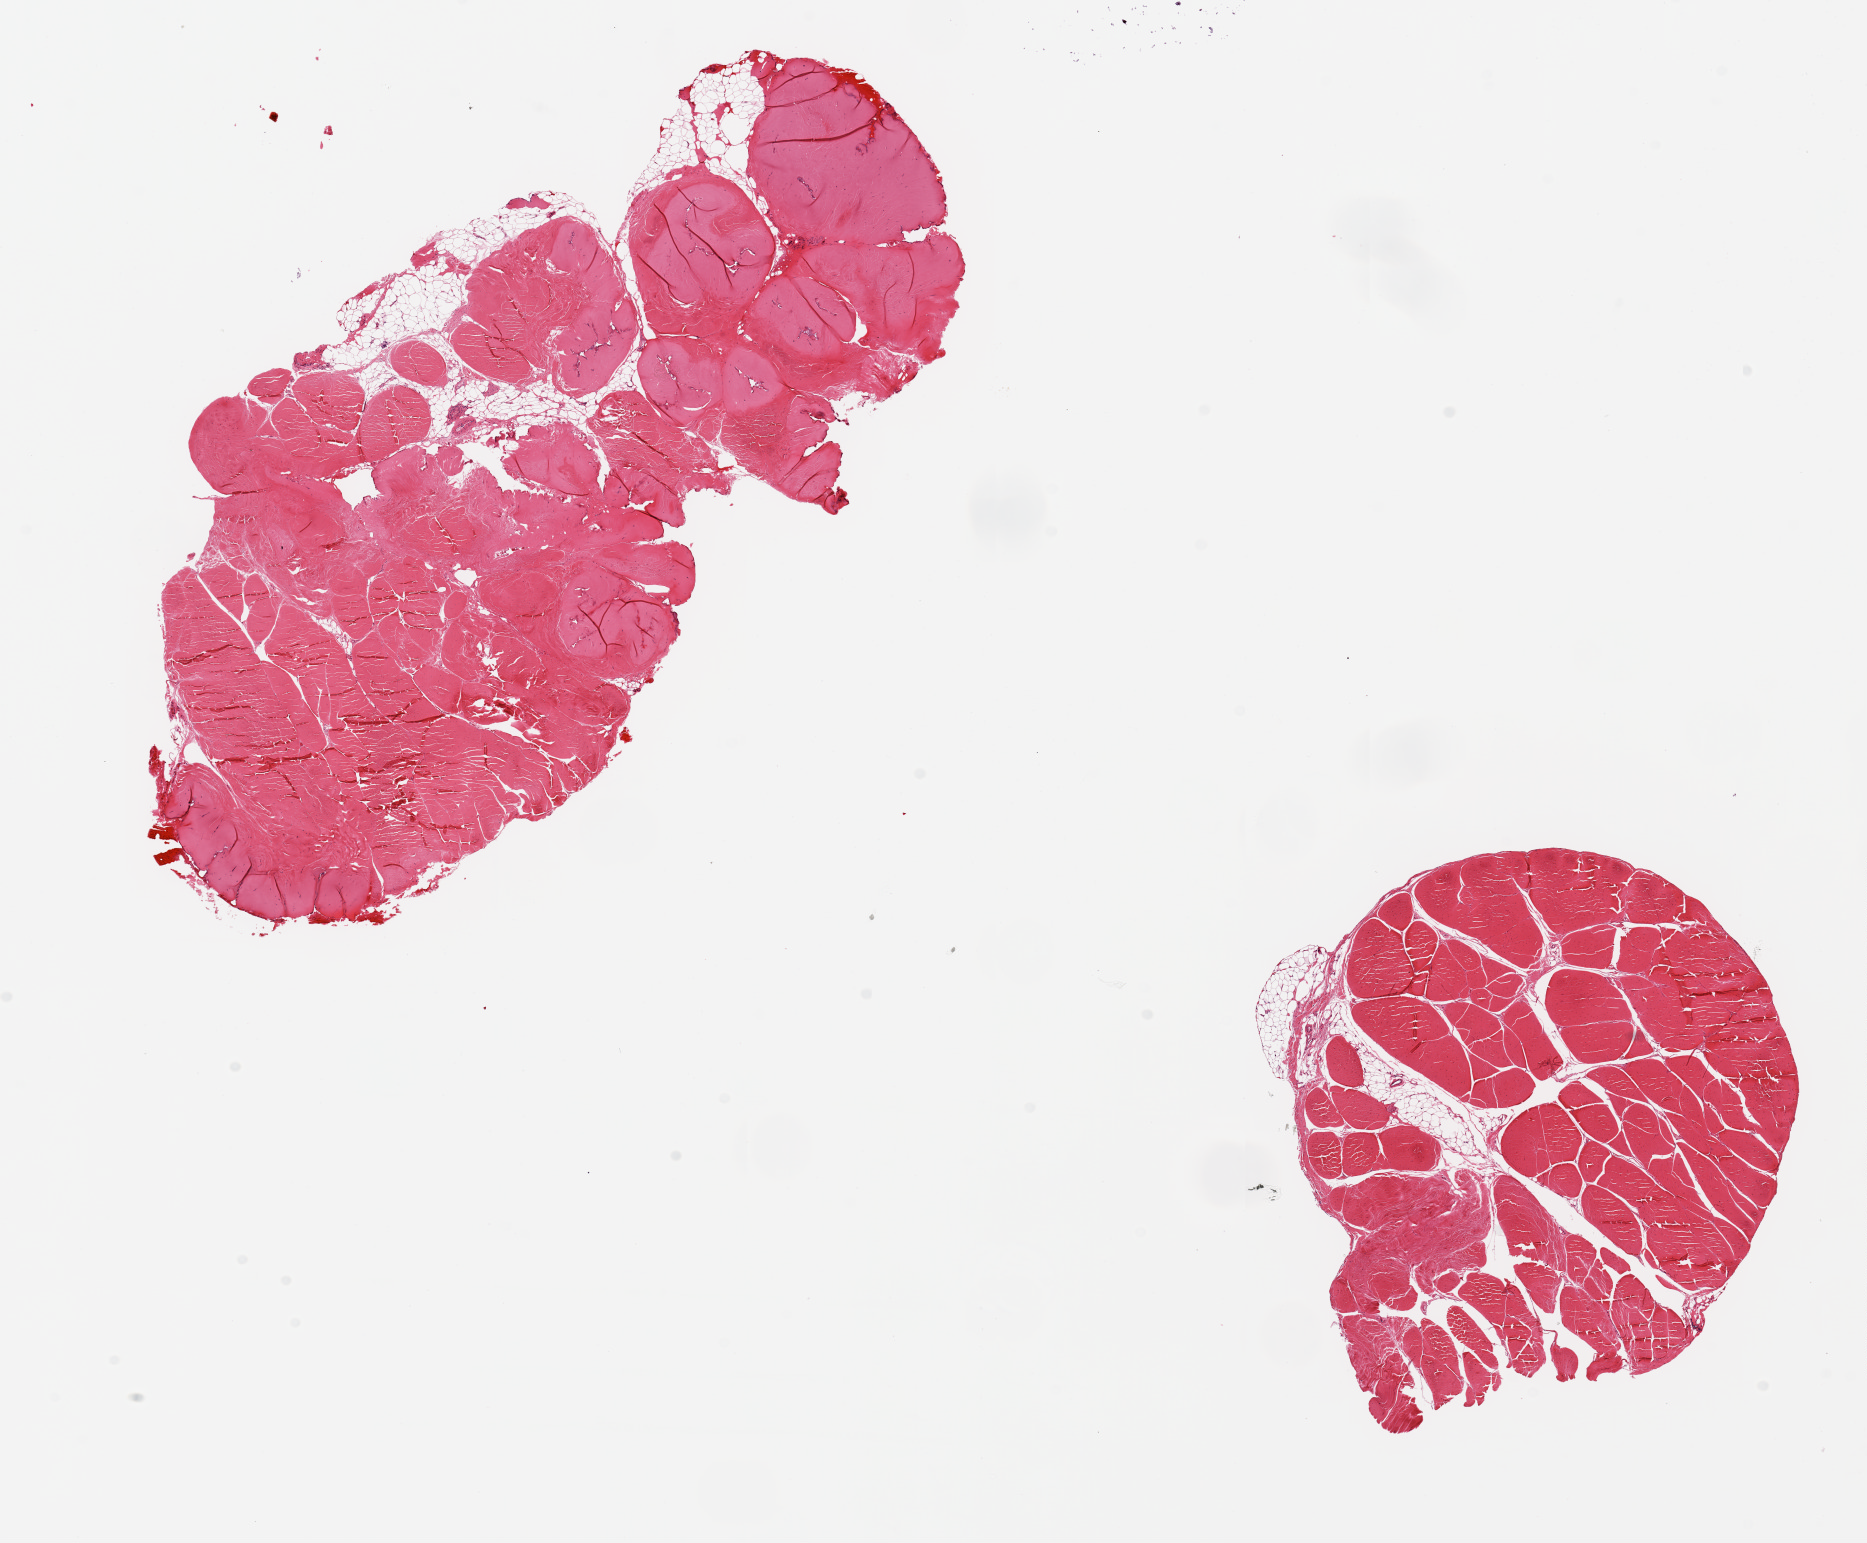
H&E whole-slide image, shown as a low-resolution overview of the whole scanned area (about 14.8 x 12.2 mm, from a 20x scan), PAXgene-fixed paraffin-embedded (PFPE) section, sampled site (target tissue): tibial nerve, donor tissue sample. Male donor.
Reviewer comment on this tissue sample: 2 pieces 8x3 & 4x4 mm; TENDON, not nerve.